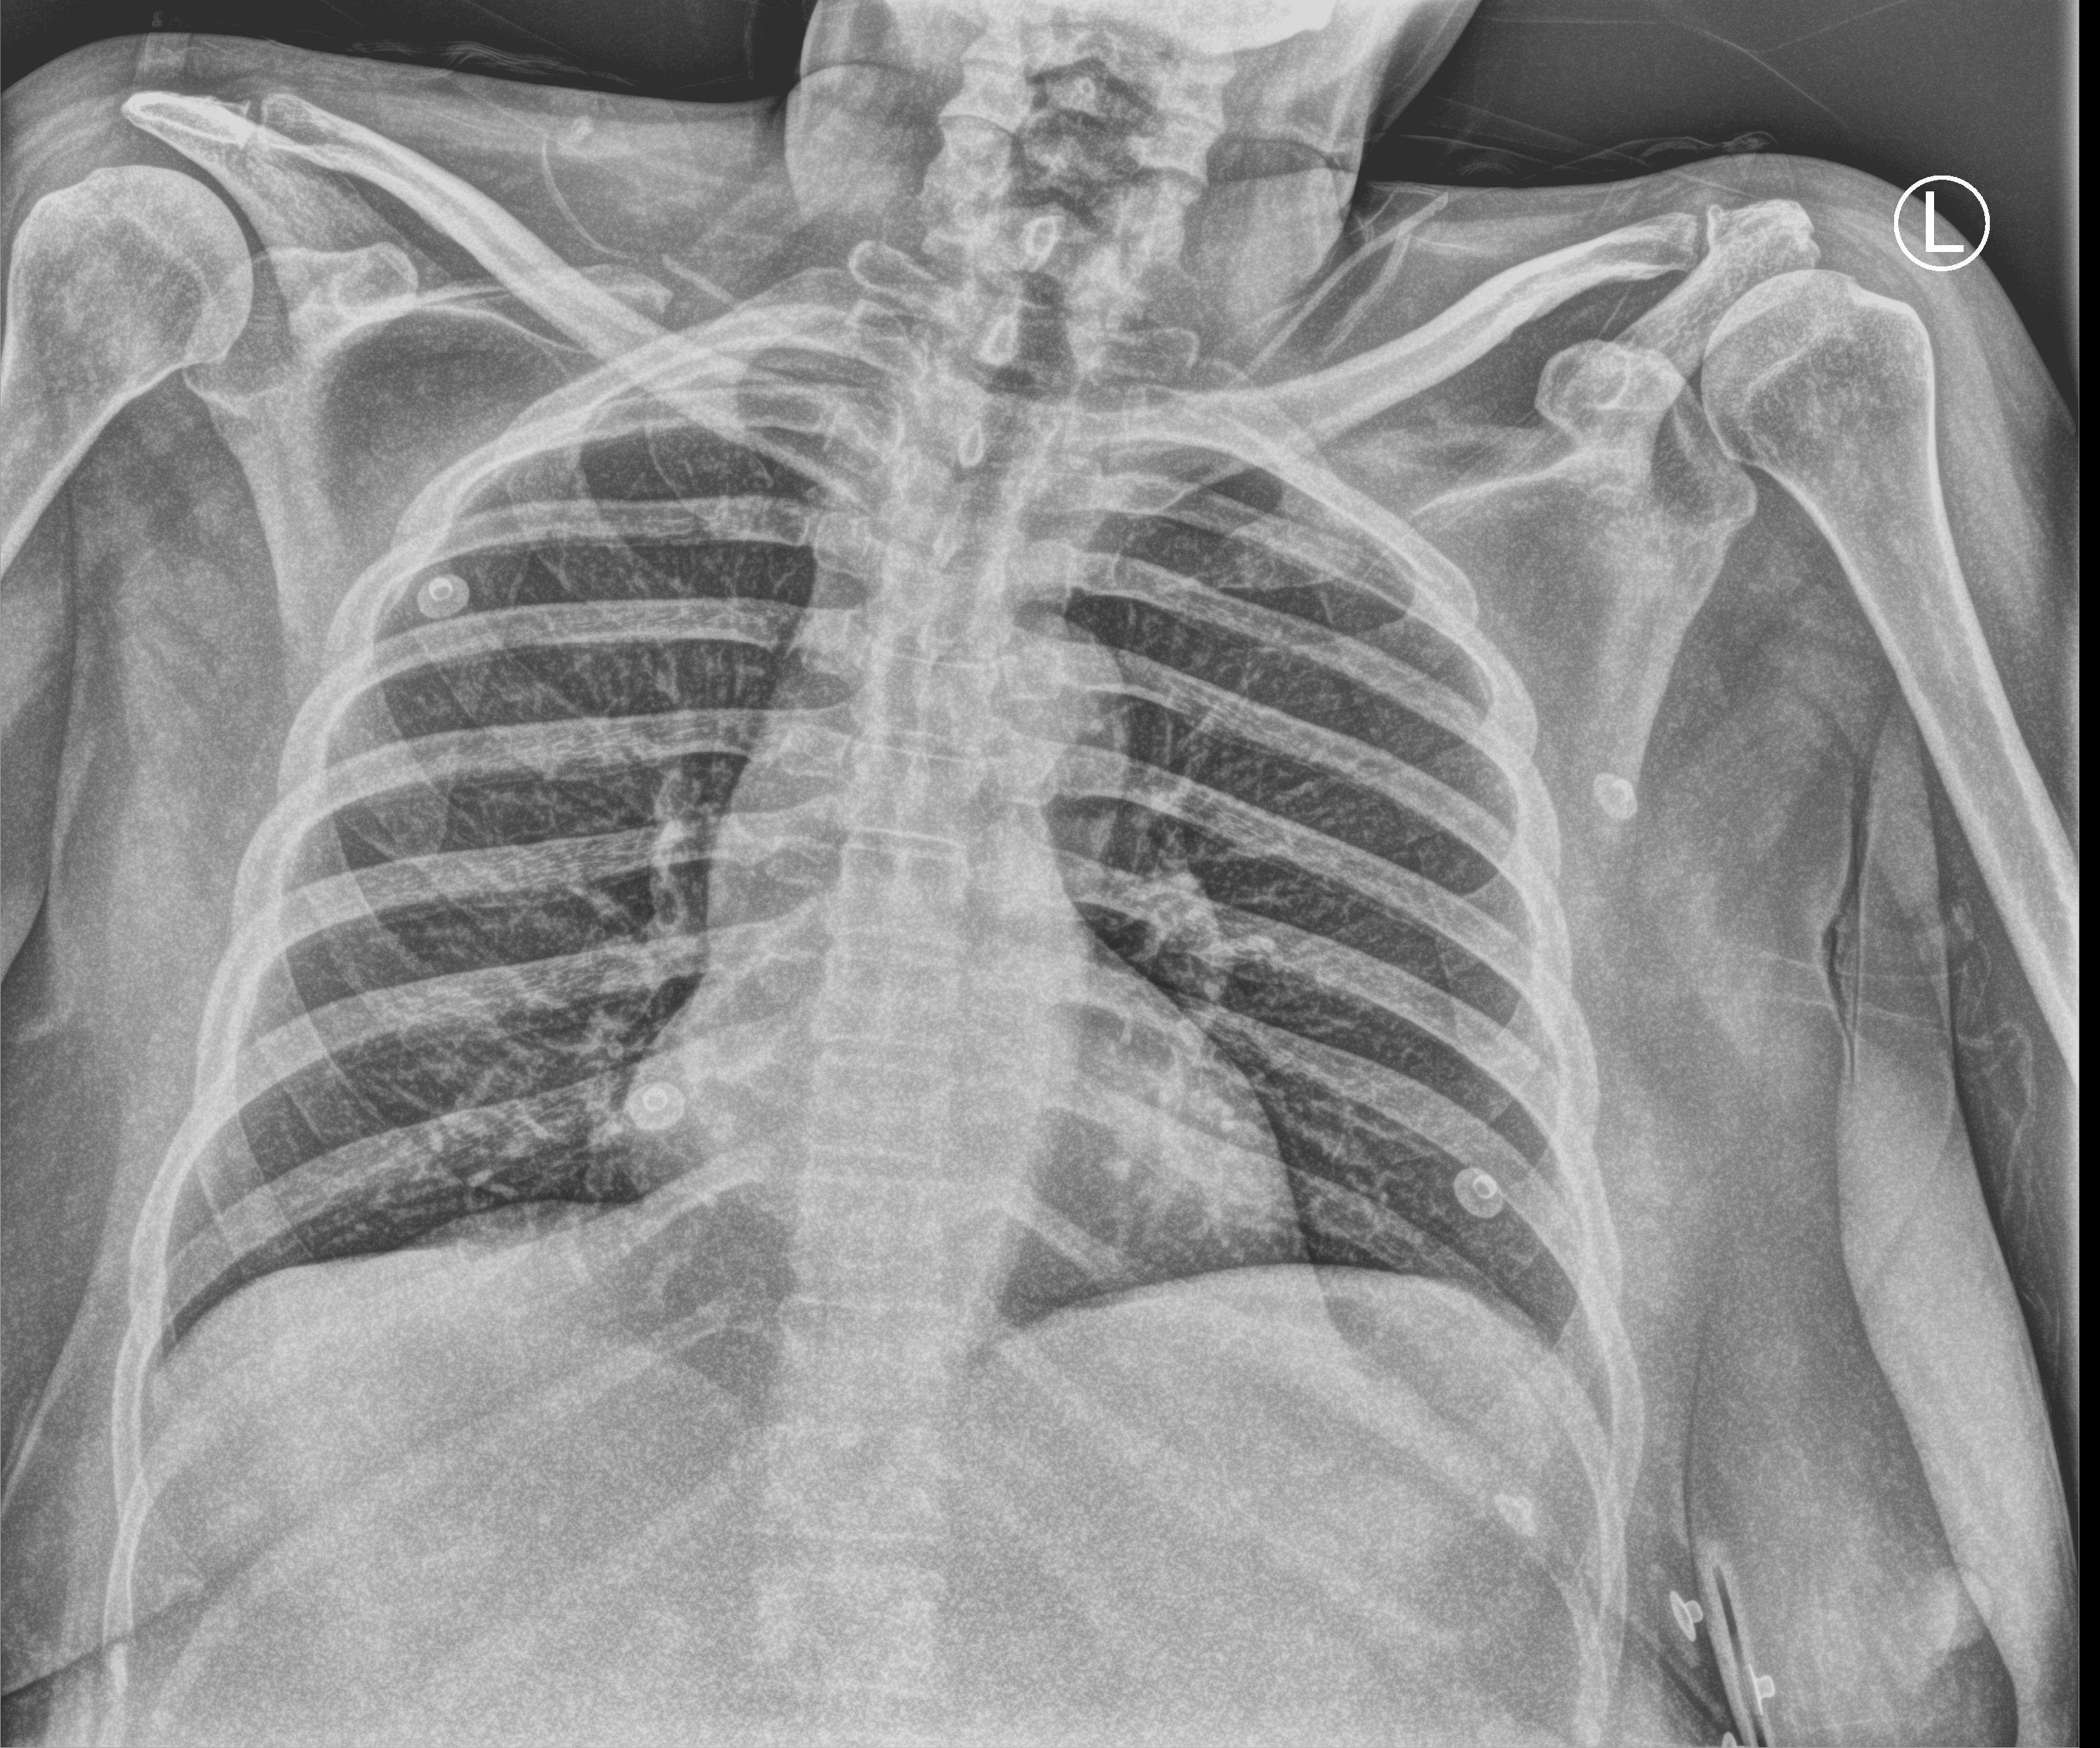
Portable chest radiograph, anteroposterior (AP) projection. Patient hospitalised with COVID-19; female, aged 18–59 years.
Hospital-stay facts (about this admission, not read from this image; timing relative to this image not recorded): smoking status (admission record): former.